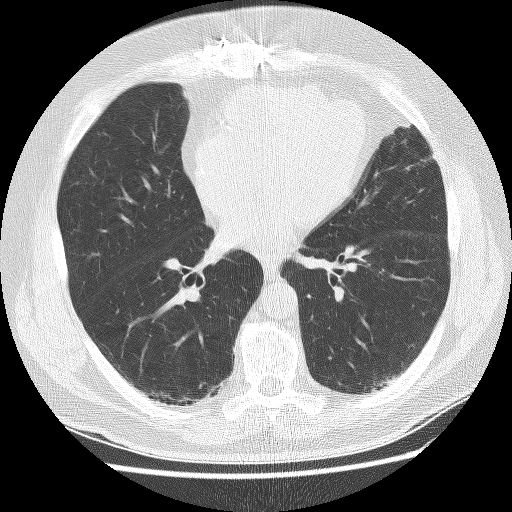
Low-dose screening chest CT, axial slice, baseline screening round, lung window (W 1500 / L -600 HU), 2.5 mm slice thickness, lung (sharp) reconstruction kernel (BONE), slice 130 of 236 in the series. Male, age 65 years at enrolment.
Expert-annotated lung lesion, bounding box [x1, y1, x2, y2] px = [355, 371, 397, 407]. No non-calcified nodule or mass ≥4 mm was recorded by the screening reader at this exam. Official screen result: negative screen, minor abnormalities not suspicious for lung cancer.